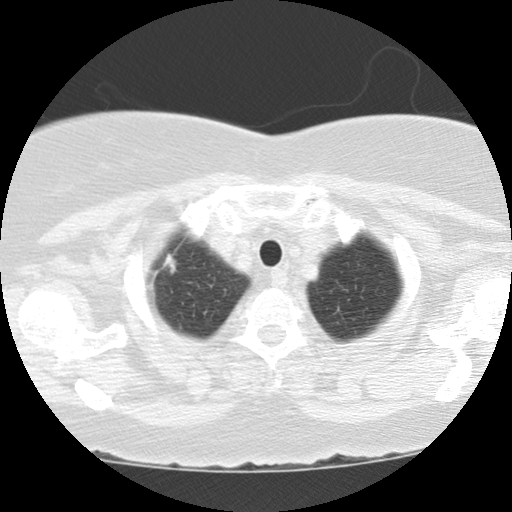
Chest CT (low-dose screening protocol), one axial image, baseline screening round, lung window (W 1500 / L -600 HU), 120 kVp, 512 × 512 image matrix, field of view 310 × 310 mm. Female, age 67 years at enrolment. Former smoker at enrolment.
Expert reader's lesion annotation, bounding box [x1, y1, x2, y2] px = [134, 237, 199, 305]. The screening reader recorded 3 non-calcified nodules or masses ≥4 mm on this exam (right upper lobe, right lower lobe, right upper lobe); which of them this box marks is not recorded.